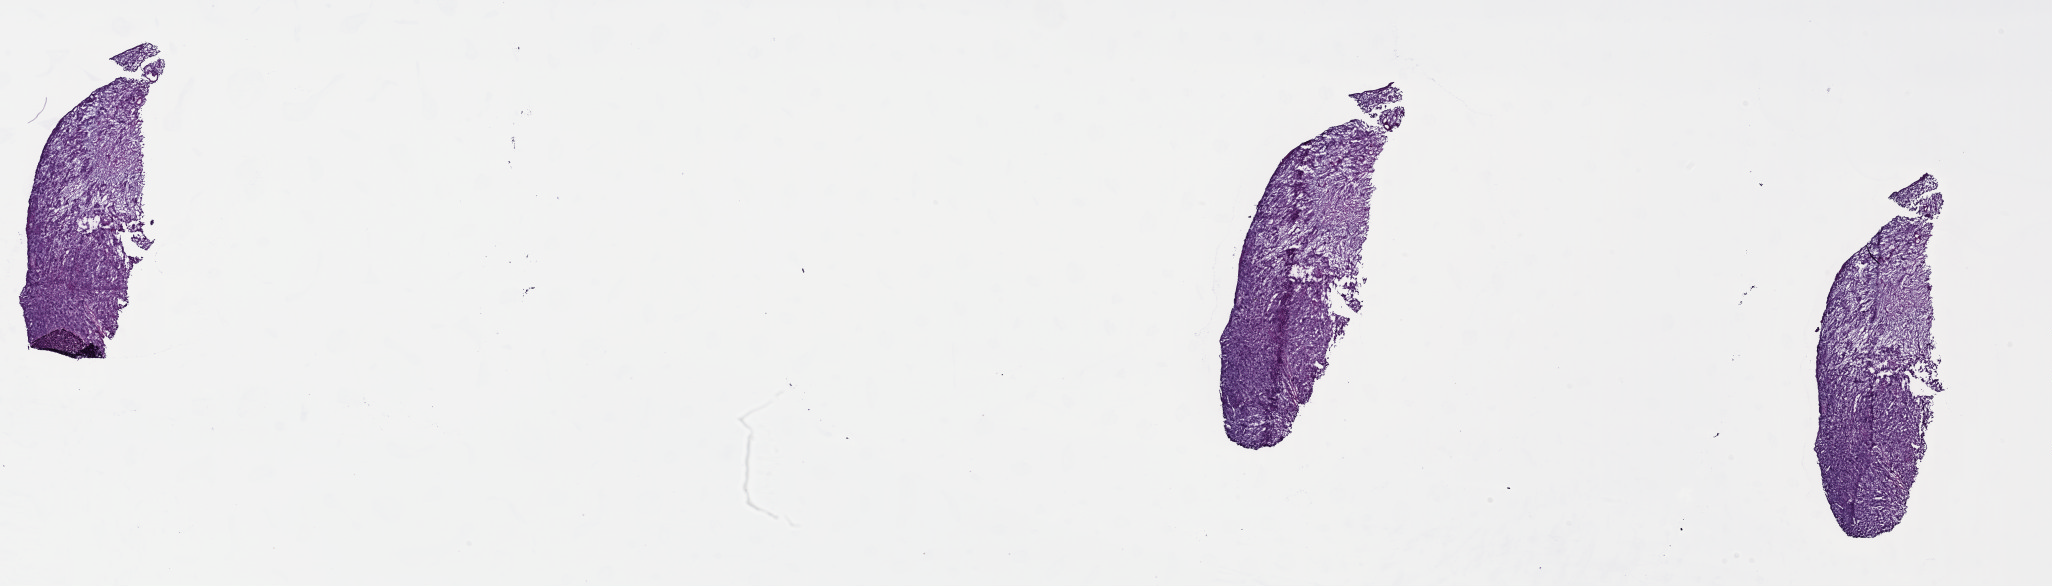
Whole-slide histology image, H&E — low-resolution overview of the scanned area, about 32.3 x 9.2 mm. Frozen section from the top of the tissue portion. Primary tumour sample from the head and neck. Female patient; age at initial diagnosis 82 years.
Pathologic diagnosis: Squamous cell carcinoma, NOS (floor of mouth, NOS).